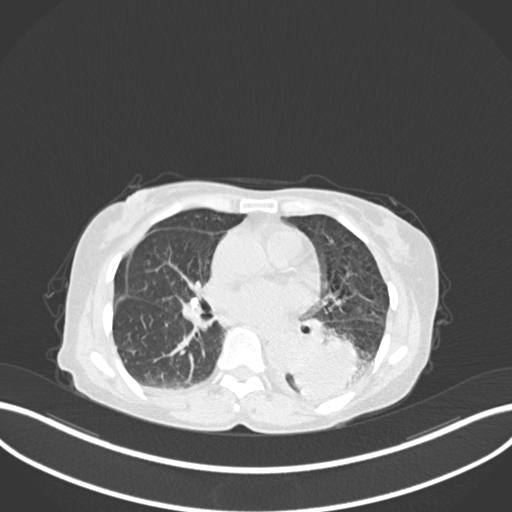
Chest CT, one axial slice; slice 76 of 233 in the series (ordered by position); reconstruction kernel B30f; lung window (W 1500 / L -600 HU); 1 mm slice thickness; 512 × 512 image matrix, field of view 400 × 400 mm. Patient: female, 78 years. From the clinical record (not read from this slice): clinical TNM (as recorded): T3 N0 M1.
Annotated regions visible in this slice (bounding box drawn by a radiologist):
- lung tumour (recorded histology: squamous cell carcinoma): box from (x=287, y=337) to (x=361, y=403) px